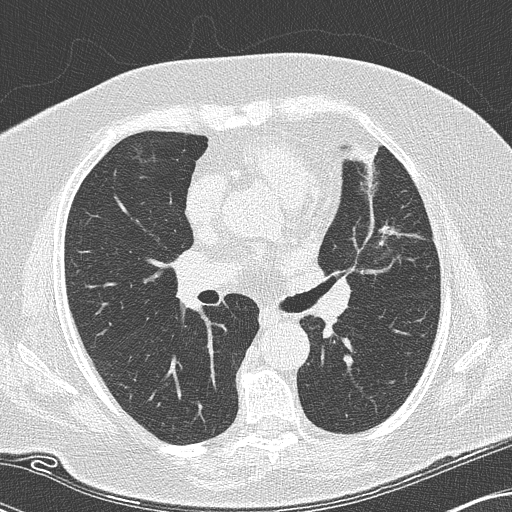
Low-dose screening chest CT, axial slice; second annual screen; lung window (W 1500 / L -600 HU); 120 kVp; slice 60 of 151 in the series; 512 × 512 image matrix. Female, age 73 years at enrolment. Current smoker at enrolment.
Expert-annotated lung lesion, bounding box <370,217,408,256> (left, top, right, bottom; pixels). The screening reader recorded 2 non-calcified nodules or masses ≥4 mm on this exam (lingula, right lower lobe); which of them this box marks is not recorded. Official screen result: positive, other.